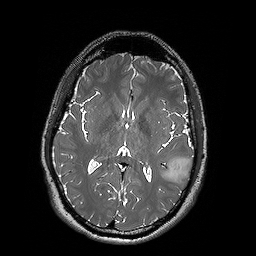
Brain MRI from a brain-tumour surgery series, one axial slice; position 87 of 192 along the scan axis; 1 mm slice thickness; 256 × 256 image matrix. Case-level facts recorded for this patient, not image findings: histopathology: Oligodendroglioma; WHO grade: 2; IDH mutation: yes; tumour location: Left Posterior Temporal.
Outlined on this slice (manually delineated by an expert):
- tumour: bounding box <159,156,193,181> (left, top, right, bottom; pixels)